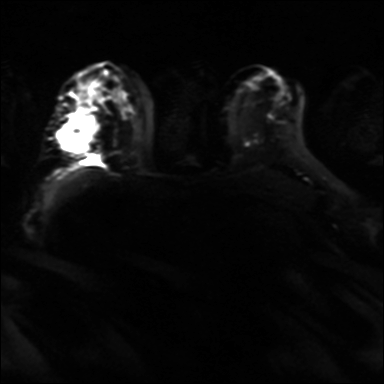
Breast MRI, one axial slice; slice 22 of 36 in the series (ordered by position); diffusion-weighted series; image 2 of 4 stored at this slice position (different b-values; order by instance number); 3 T; 4 mm slice thickness; 384 × 384 image matrix, field of view 320 × 320 mm. Female patient.
Structures marked on this image (expert manual segmentation):
- tumour on diffusion-weighted imaging: bounding box (x1, y1, x2, y2) in pixels: (60, 116, 98, 153)